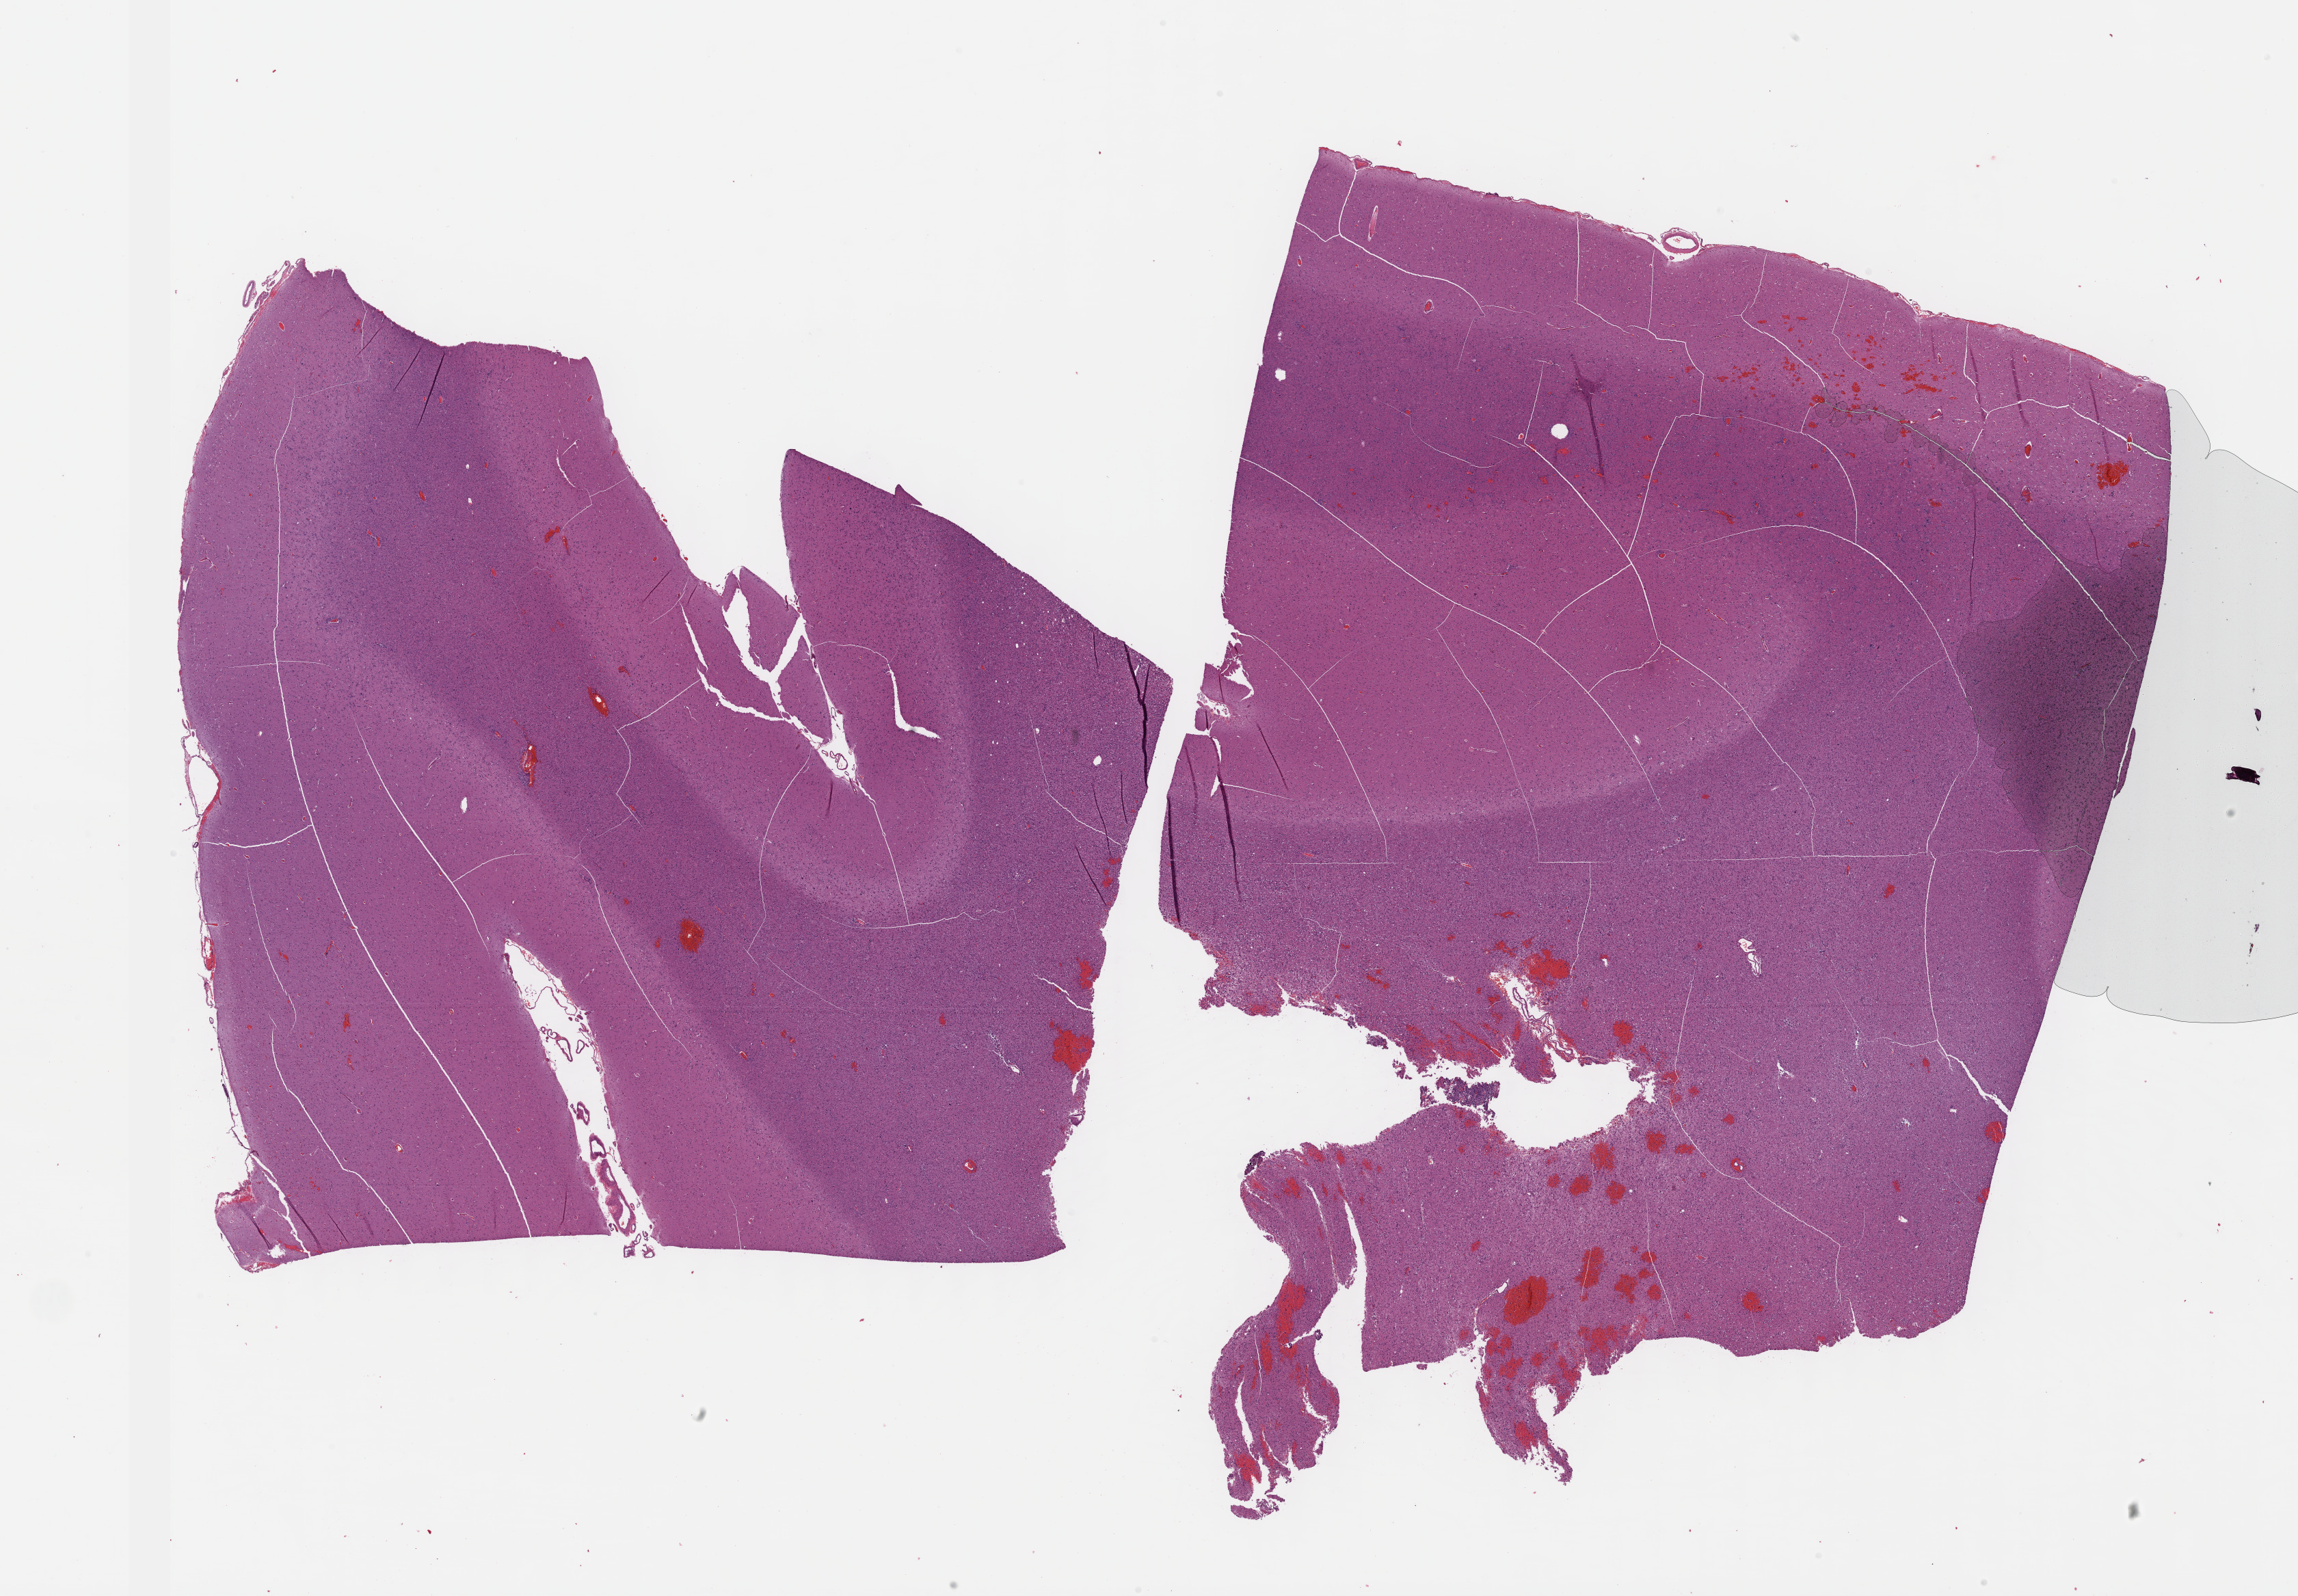
Hematoxylin and eosin (H&E) stained whole-slide image — shown as a low-resolution overview of the whole scanned area (about 27.2 x 18.9 mm), FFPE section, brain, primary tumour sample. Male, age 59 years at initial diagnosis. Histologic grade: G3 (poorly differentiated).
Laterality: left. Diagnosis: Oligodendroglioma, anaplastic.